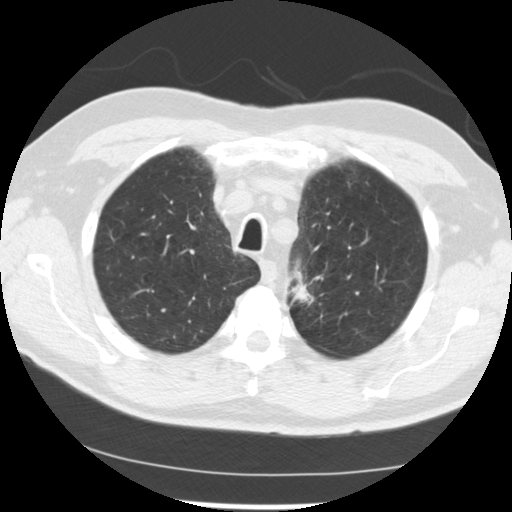
Axial slice from a low-dose chest CT screening exam. First (baseline) screen. Lung window (W 1500 / L -600 HU). 2.5 mm slice thickness. Standard (soft-tissue) reconstruction kernel (STANDARD). Slice 198 of 249 in the series. Male, age 71 years at enrolment.
Expert reader's lesion annotation, bounding box (x1, y1, x2, y2) in pixels: (275, 260, 334, 316). The screening reader recorded 2 non-calcified nodules or masses ≥4 mm on this exam; which of them this box marks is not recorded. Official screen result: positive, change unspecified: nodule(s) >= 4 mm or enlarging nodule(s), mass(es), or other non-specific abnormalities suspicious for lung cancer.